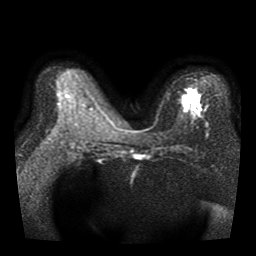
Breast MRI, one axial slice; slice 19 of 40 in the series (ordered by position); diffusion-weighted series; image 2 of 4 stored at this slice position (different b-values; order by instance number); 1.5 T; 5 mm slice thickness; 256 × 256 image matrix. Female patient.
Structures marked on this image (expert manual segmentation):
- tumour on diffusion-weighted imaging: box from (x=180, y=88) to (x=202, y=104) px